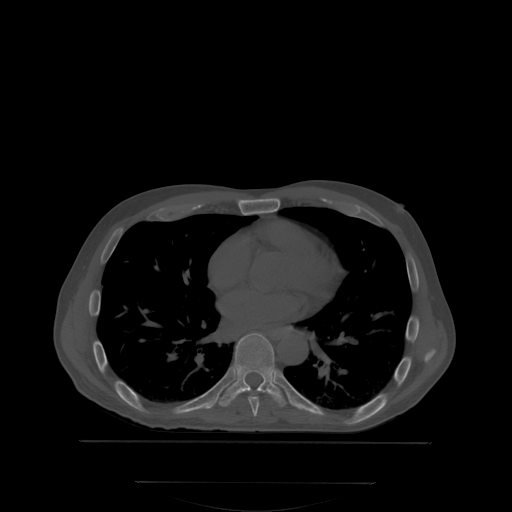
CT including the spine, one axial slice; slice 219 of 350 in the series (ordered by position); bone window (W 1800 / L 400 HU); 2.5 mm slice thickness; 512 × 512 image matrix, field of view 500 × 500 mm. Patient: male, 58 years. From the clinical record (not read from this slice): primary cancer: prostate.
Structures marked on this image (semi-automatically segmented with operator editing):
- T7 vertebra: box from (x=249, y=396) to (x=259, y=417) px
- T8 vertebra: (x=218, y=333)–(x=287, y=408)